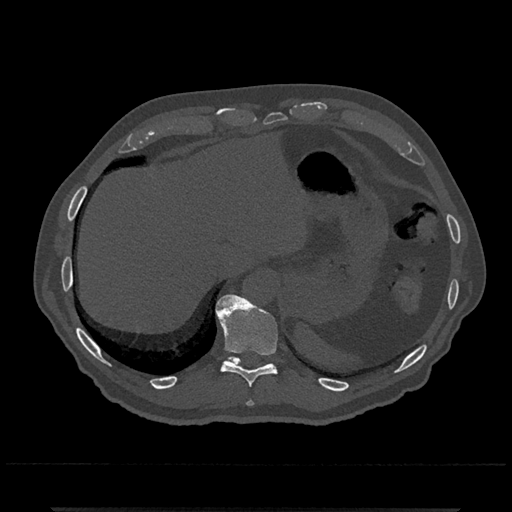
CT including the spine, one axial slice; slice 545 of 797 in the series (ordered by position); reconstruction kernel Br40s/3; 120 kVp; bone window (W 1800 / L 400 HU); 0.5 mm slice thickness; 512 × 512 image matrix, field of view 393 × 393 mm. Male patient, age 67 years. From the clinical record (not read from this slice): primary cancer: prostate.
Outlined on this slice (semi-automatic segmentation, software-assisted and operator-edited):
- T10 vertebra: bounding box (x1, y1, x2, y2) in pixels: (215, 294, 278, 387)
- T11 vertebra: (227, 356, 271, 367)
- T9 vertebra: (247, 401, 254, 406)